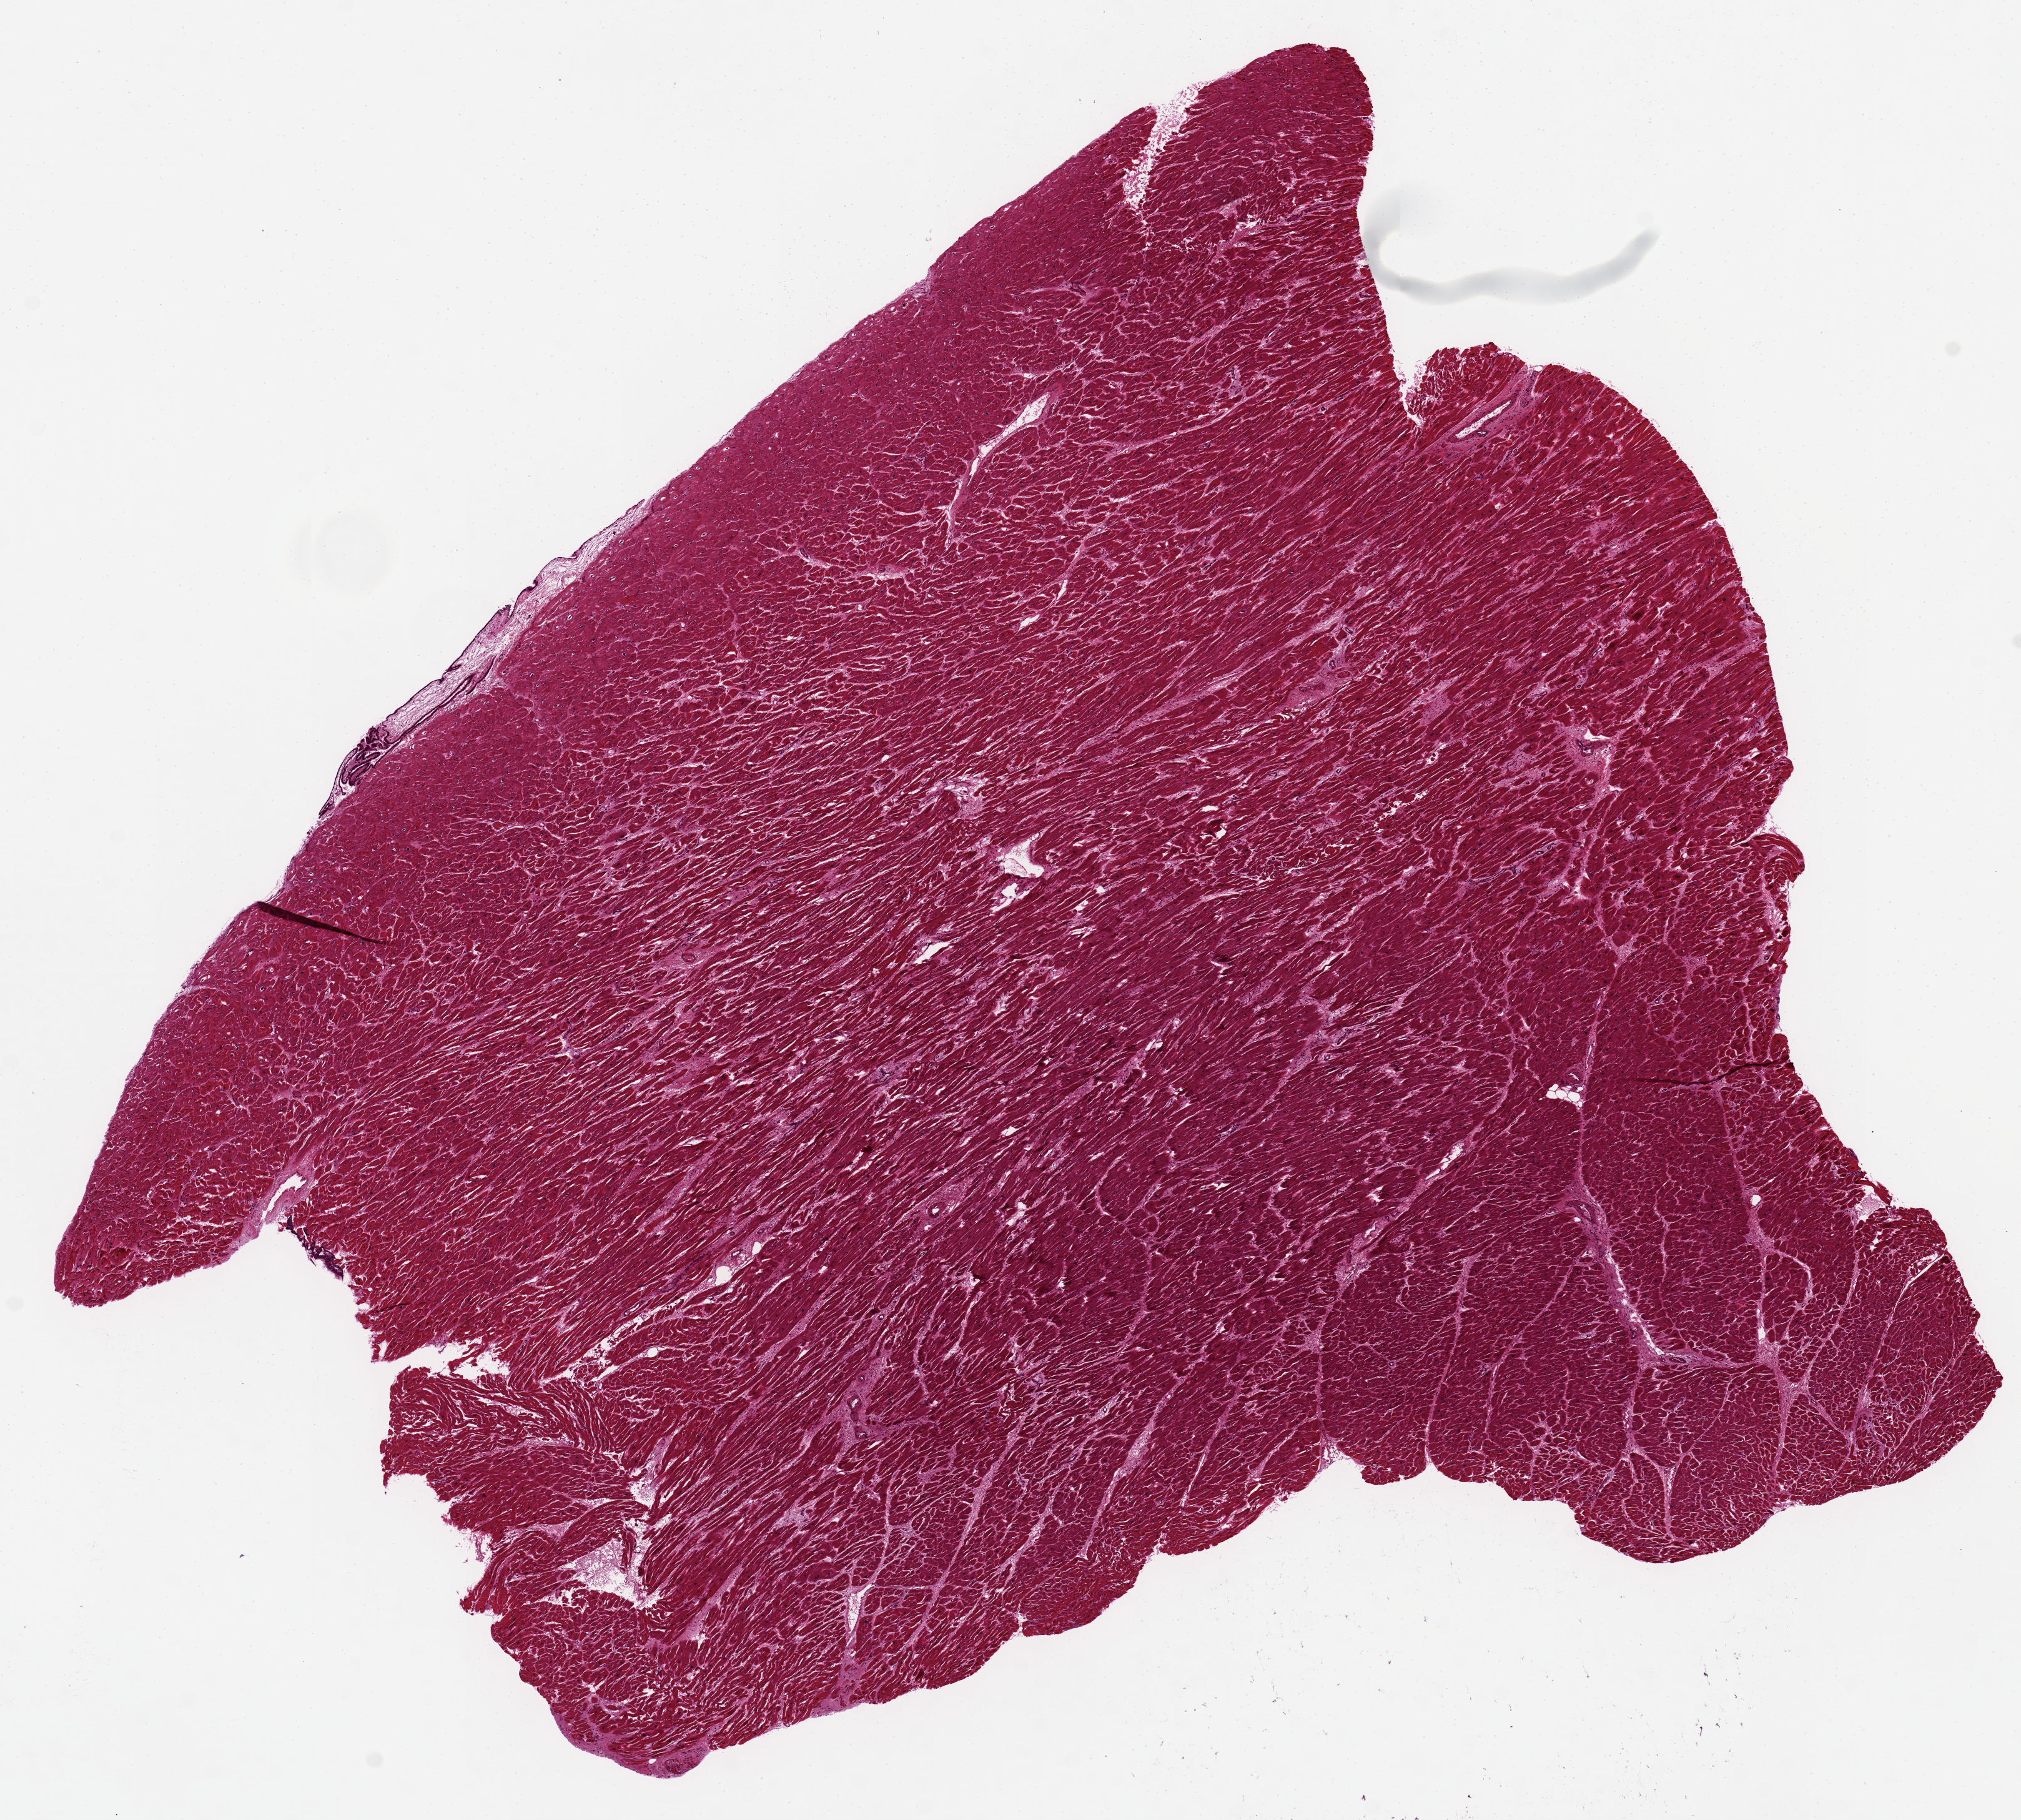
H&E whole-slide image, brightfield — whole scanned area (about 12.8 x 11.5 mm) shown as a low-resolution overview; PAXgene-fixed paraffin-embedded (PFPE) section; section of heart (target tissue); donor tissue sample. Donor: male.
• pathologist's review note for this sample: minimal interstitial fibrosis